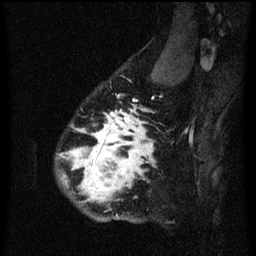
Breast MRI (dynamic contrast-enhanced), one sagittal slice. Slice 51 of 60 in the series (ordered by position). Dynamic contrast-enhanced series, image 2 of 3 at this slice position (ordered by acquisition). 1.5 T. TE 4.2 ms, TR 8.4 ms. 256 × 256 image matrix, field of view 180 × 180 mm. Female patient, age 34 years. Case-level facts recorded for this patient, not image findings: setting: breast cancer imaged before/during neoadjuvant chemotherapy; receptor status: HR-positive, HER2-negative.
Annotated regions visible in this slice (semi-automatic segmentation, software-assisted and operator-edited):
- analysis volume of interest (the breast-tissue region the enhancement analysis was run in; not a lesion): bounding box (x1, y1, x2, y2) in pixels: (58, 58, 173, 225)
- tumour enhancement mask (voxels above the 70 % enhancement threshold inside the analysis volume of interest): (62, 106, 153, 203)